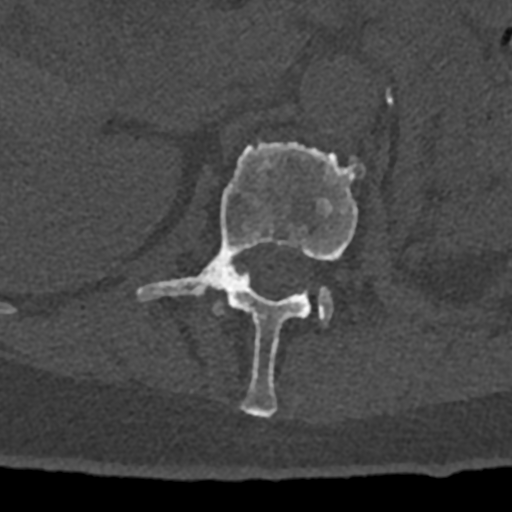
CT including the spine, one axial slice. Slice 426 of 797 in the series (ordered by position). 120 kVp. Bone window (W 1800 / L 400 HU). 512 × 512 image matrix, field of view 160 × 160 mm. Patient: male, 74 years. From the clinical record (not read from this slice): primary cancer: renal.
Outlined on this slice (semi-automatically segmented with operator editing):
- L1 vertebra: bounding box <136,141,364,418> (left, top, right, bottom; pixels)
- L2 vertebra: <215,292,332,325>